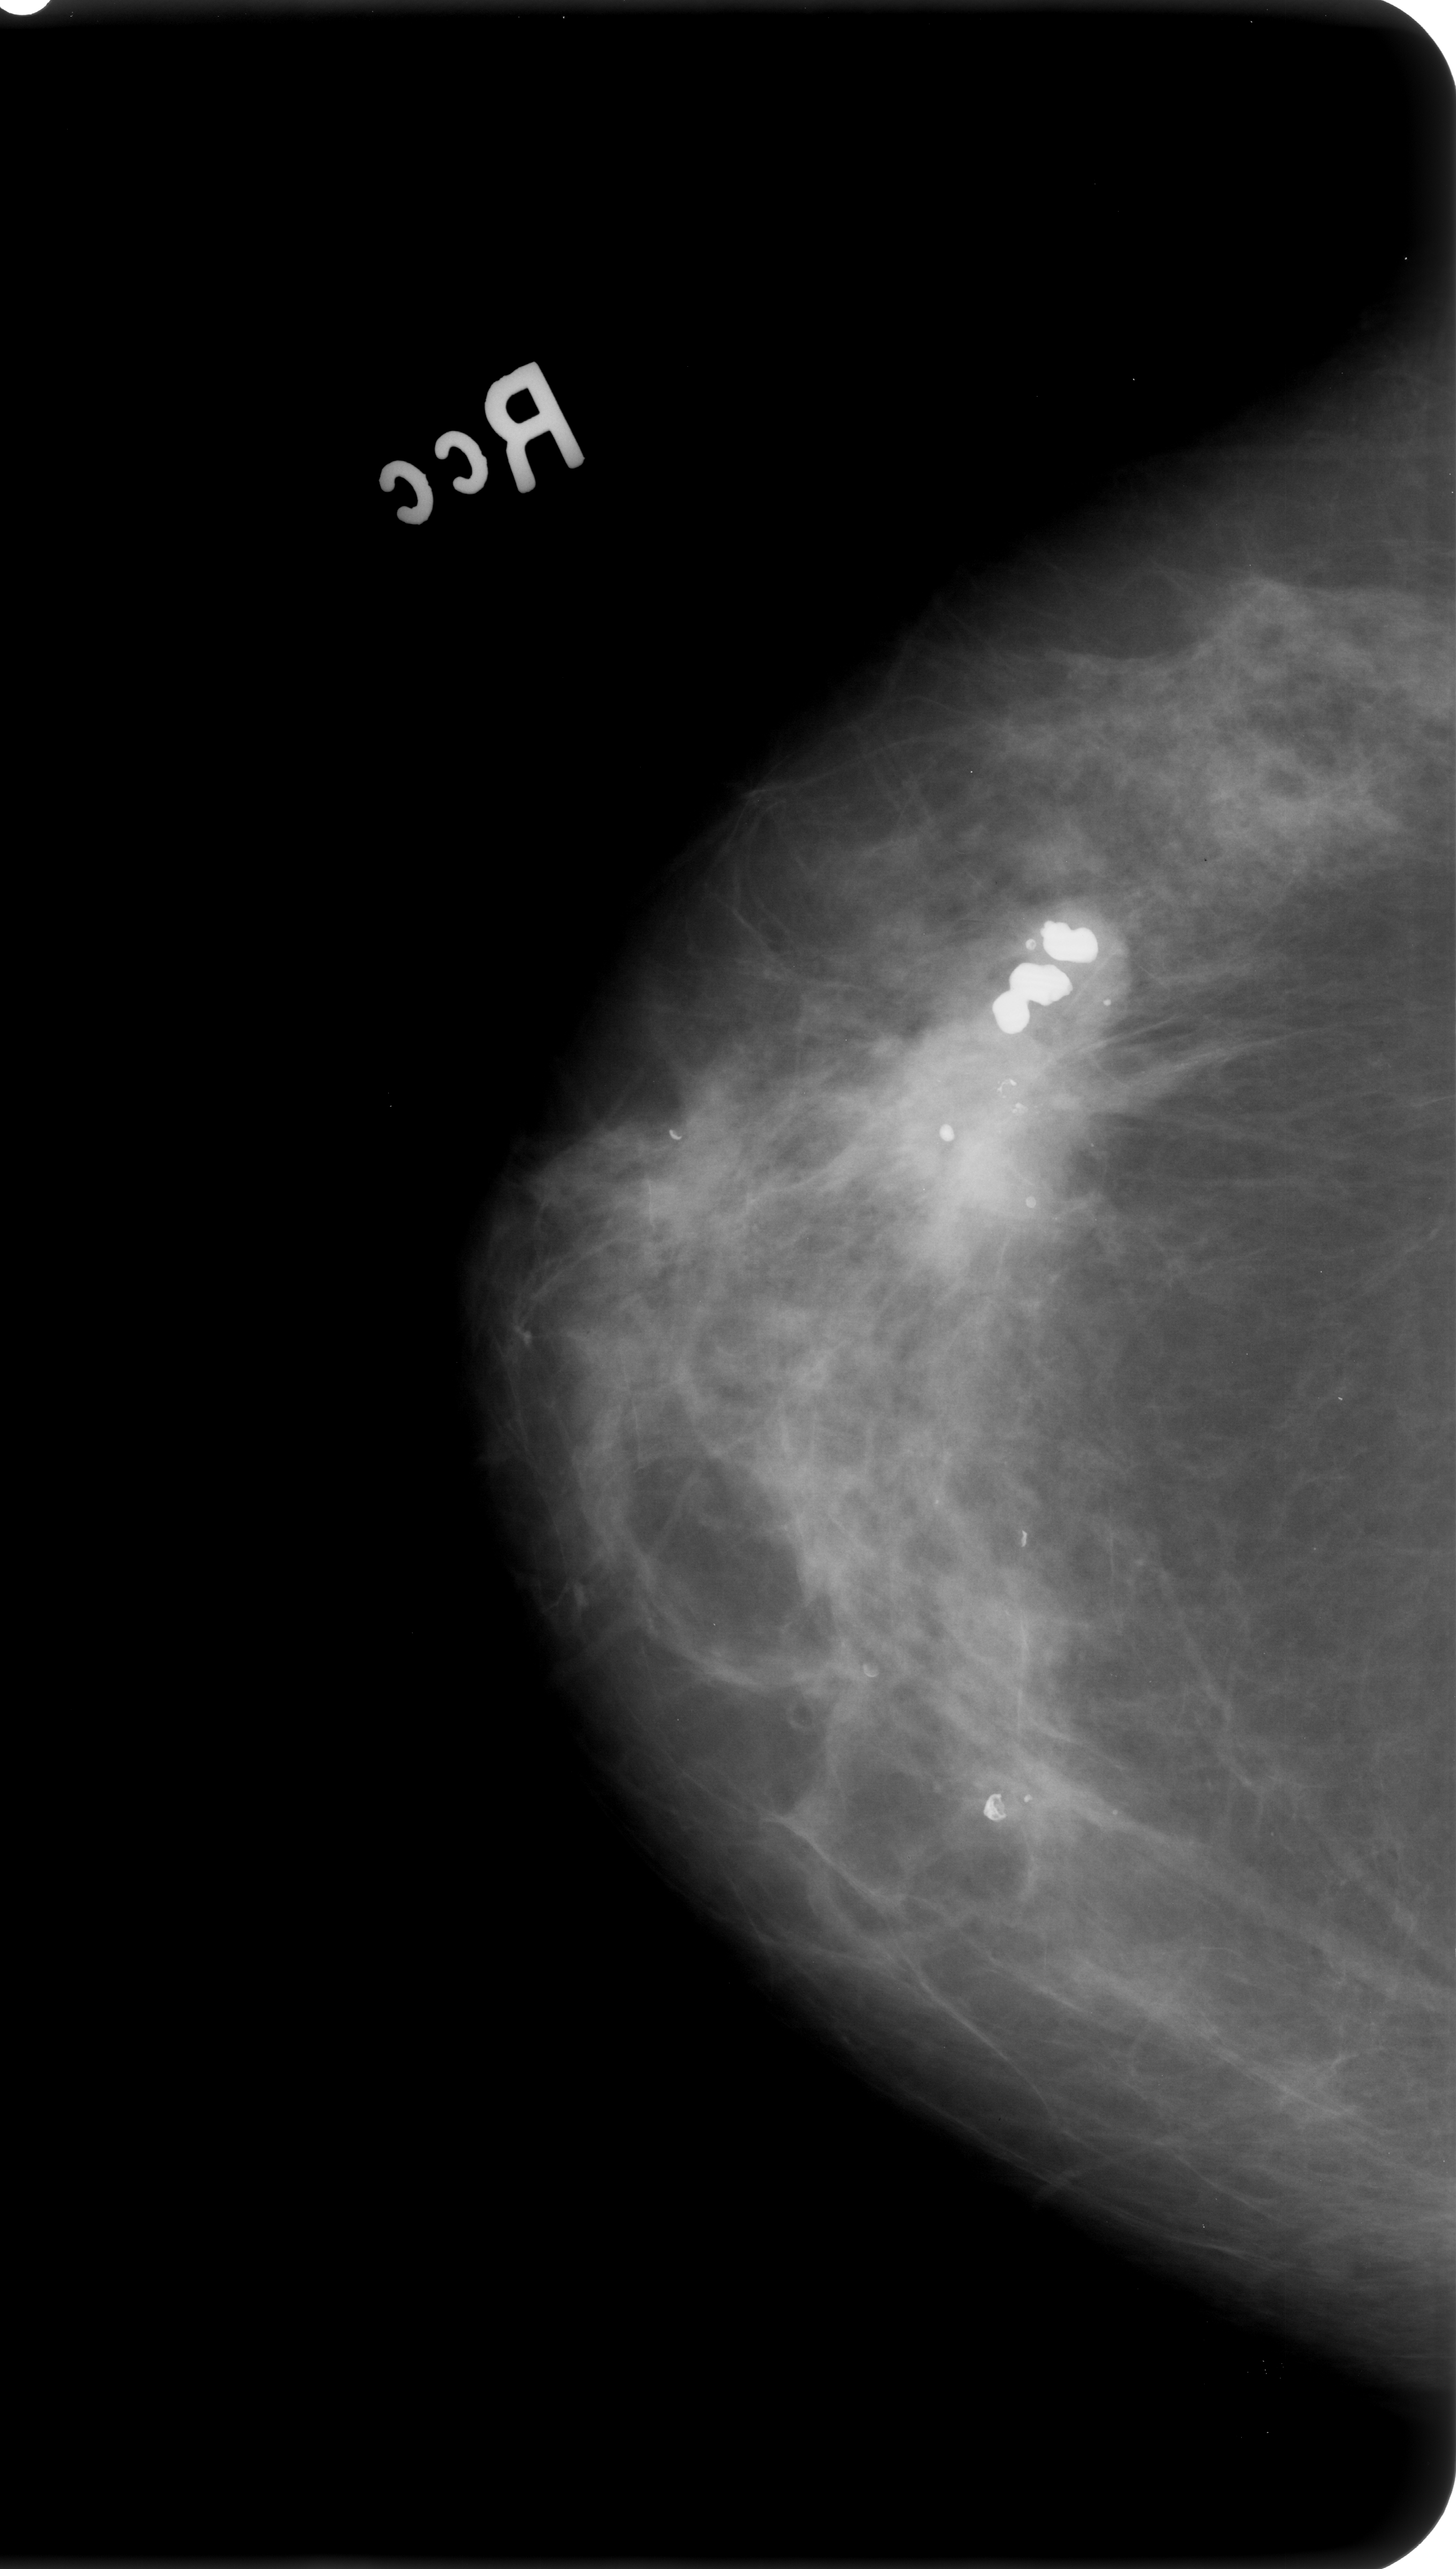
Mammogram (digitized film); right breast; CC view; breast composition: heterogeneously dense (BI-RADS density category 3 of 4).
Abnormality record for this image: Finding 1 of 2: calcifications, morphology pleomorphic, distribution clustered; BI-RADS assessment category 4; subtlety rating 4 on a 1 (subtle) to 5 (obvious) scale; pathology (as recorded): malignant. Finding 2 of 2: calcifications, morphology pleomorphic, distribution clustered; BI-RADS assessment category 4; subtlety rating 4 on a 1 (subtle) to 5 (obvious) scale; pathology result (as recorded, not read from the image): malignant.